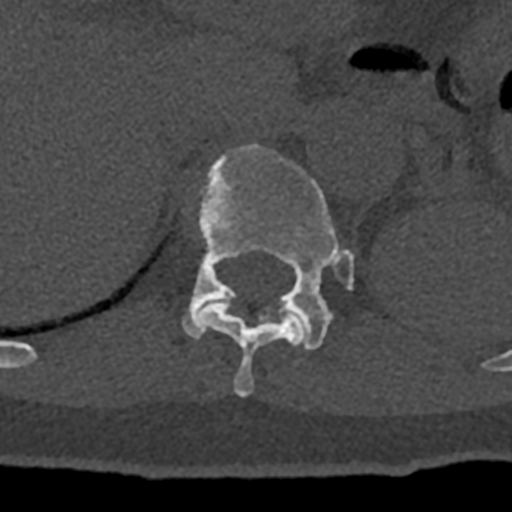
CT including the spine, one axial slice. Slice 517 of 797 in the series (ordered by position). Reconstruction kernel Br40s/3. 120 kVp. Bone window (W 1800 / L 400 HU). 0.5 mm slice thickness. 512 × 512 image matrix. Patient: male, 74 years. Case-level facts recorded for this patient, not image findings: primary cancer: renal; vertebrae with lytic lesions (as recorded): T10, L1, L2, L3, L4, L5.
Annotated regions visible in this slice (semi-automatic segmentation, software-assisted and operator-edited):
- T11 vertebra: bounding box <195,302,306,397> (left, top, right, bottom; pixels)
- T12 vertebra: <182,143,354,350>